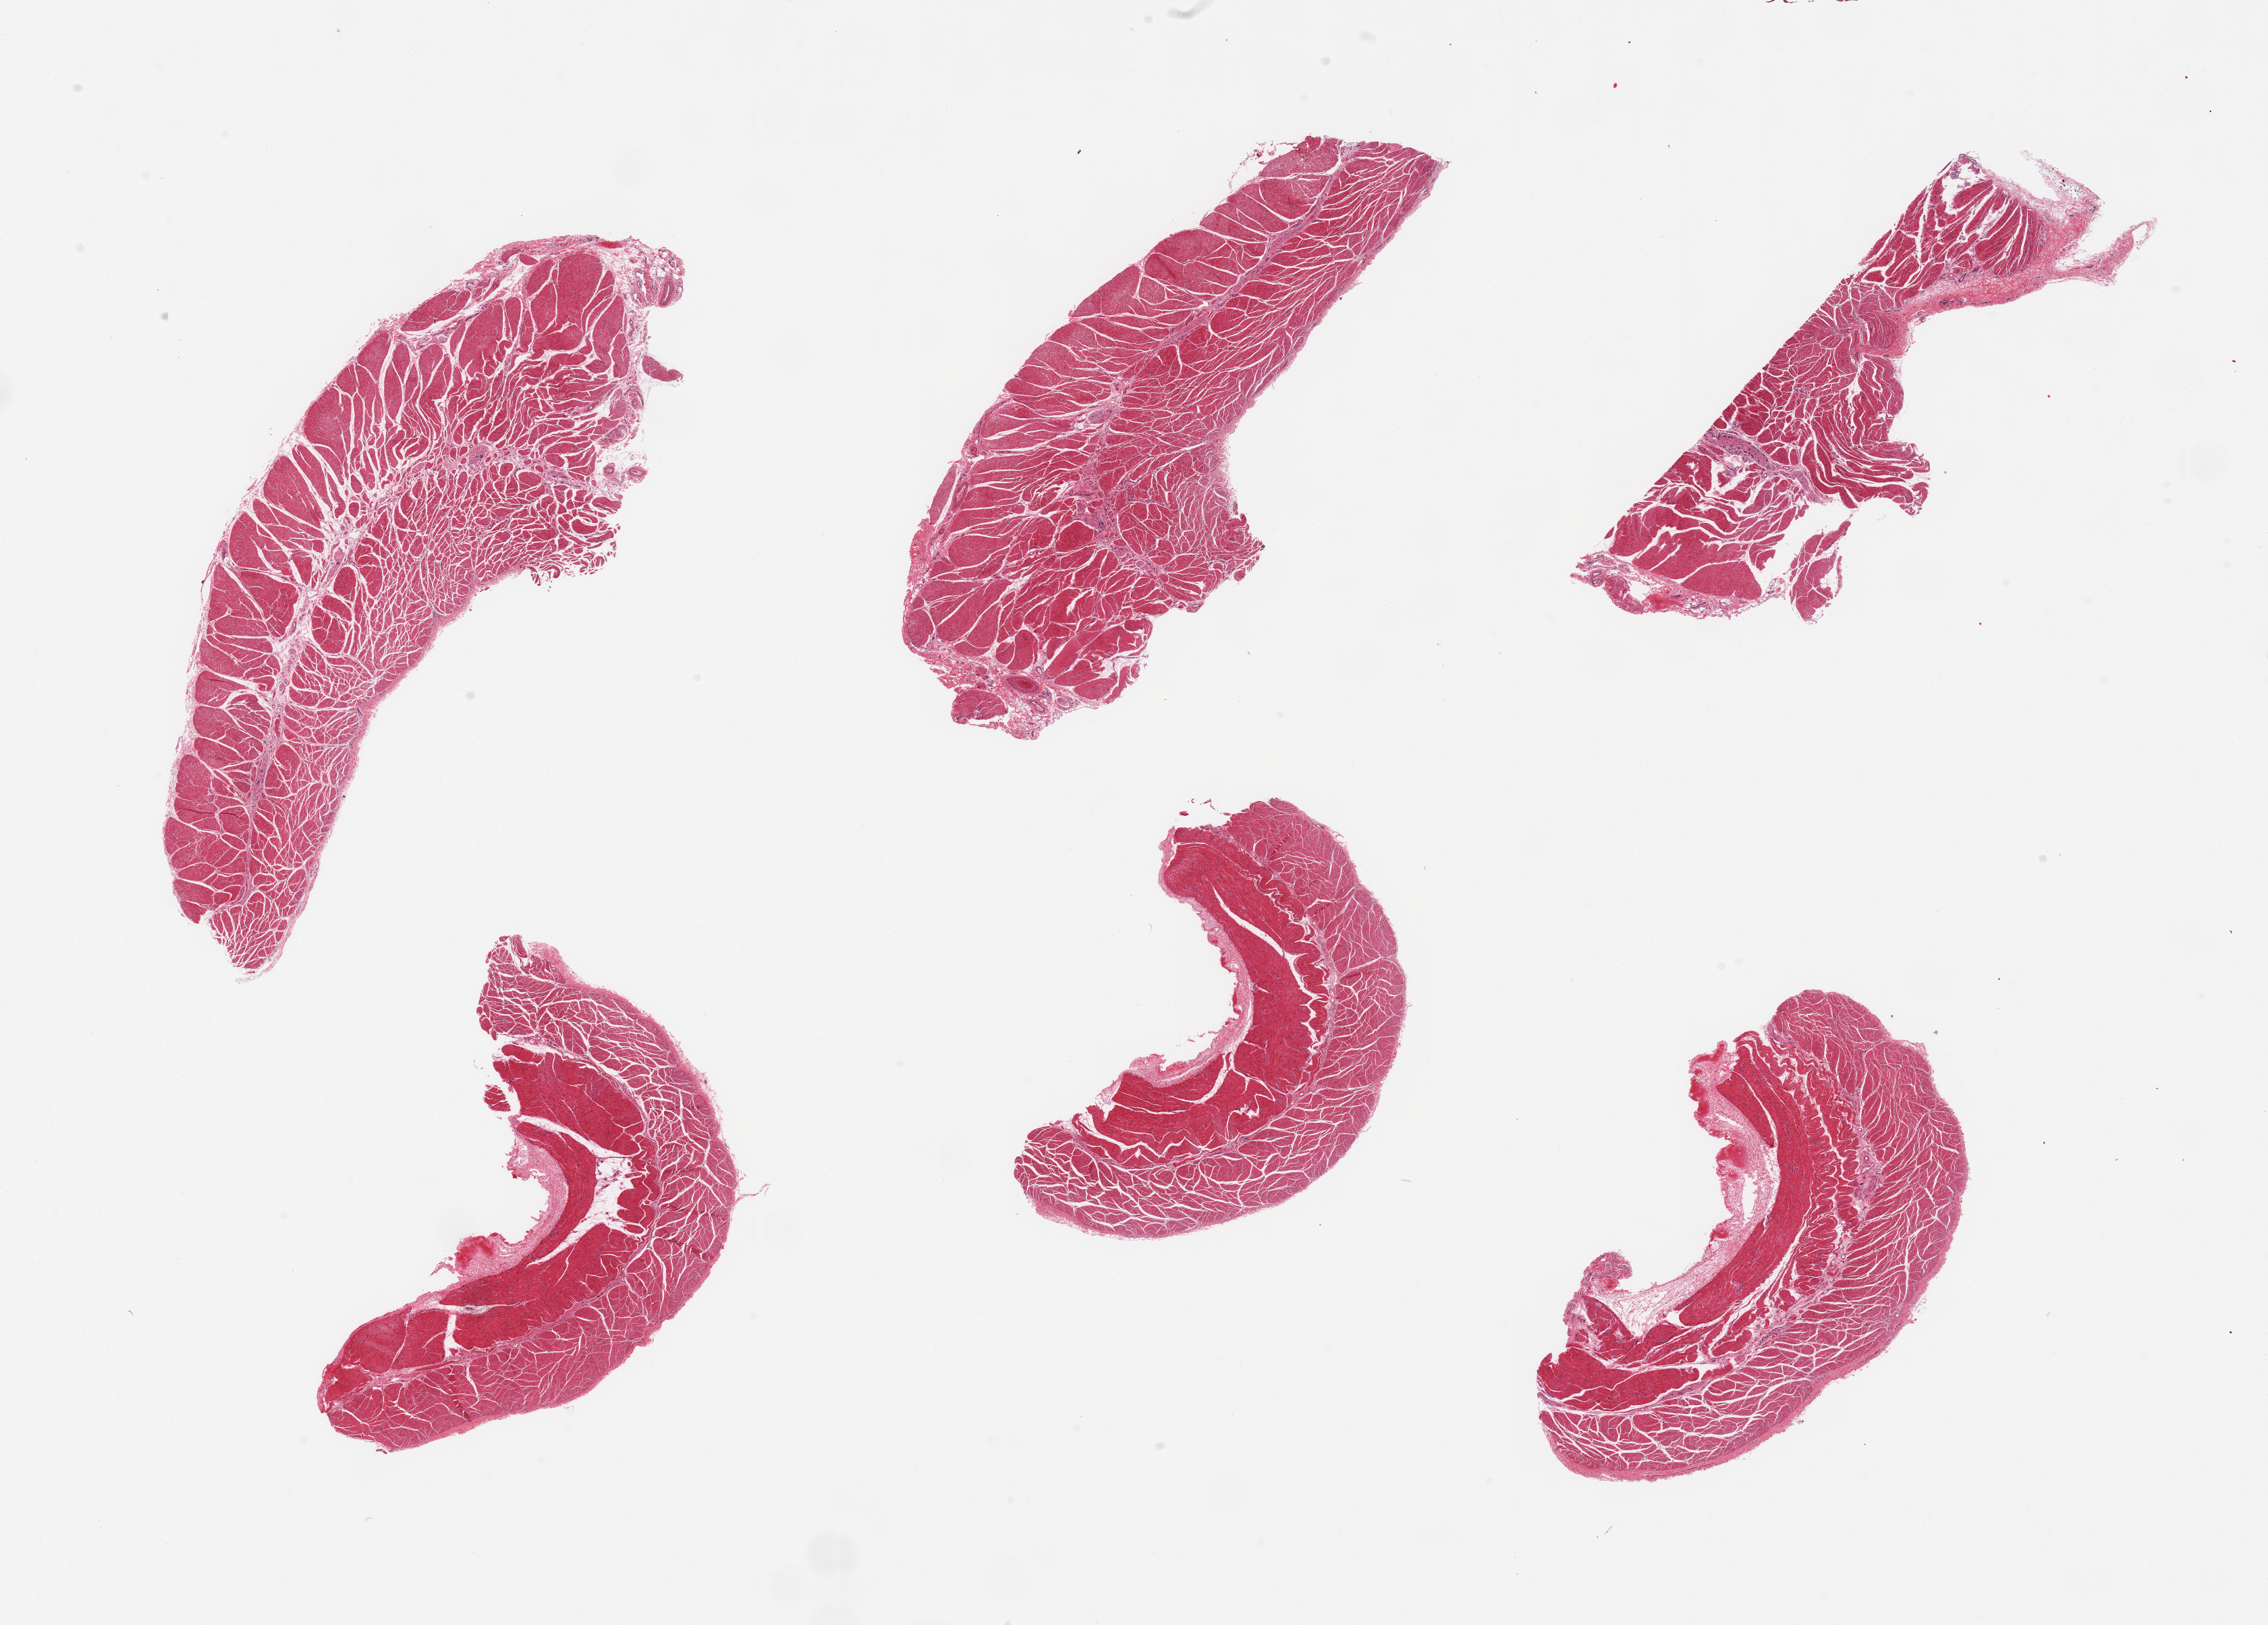
Digitized hematoxylin and eosin (H&E)-stained section, brightfield, low-resolution overview of the scanned area, about 26.6 x 19.0 mm, PAXgene-fixed paraffin-embedded (PFPE) section, sampled site (target tissue): esophageal muscle, tissue donor sample. Donor: female.
* reviewer comment on this tissue sample: 6 pieces; rare crystalline structures in small amount of submucosa, as described in the stomach